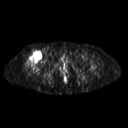
FDG PET of an extremity soft-tissue mass (from a PET/CT study), one axial slice; position 280 of 311 along the scan axis; 3.27 mm slice thickness; 128 × 128 image matrix, field of view 500 × 500 mm. Female patient, age 57 years. From the clinical record (not read from this slice): histological type: pleiomorphic undifferentiated sarcoma; grade: high; site of the primary tumour: right quadricep.
Annotated regions visible in this slice (expert contour drawn on MRI and transferred to this co-registered scan by the dataset authors):
- tumour plus oedema (research contour): box from (x=25, y=50) to (x=42, y=68) px
- tumour (research contour): (x=25, y=50)–(x=42, y=67)